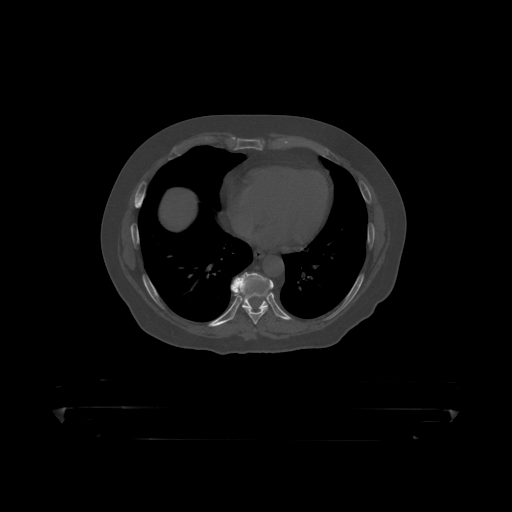
CT including the spine, one axial slice; position 249 of 390 along the scan axis; reconstruction kernel STANDARD; 120 kVp; bone window (W 1800 / L 400 HU); 1.25 mm slice thickness; 512 × 512 image matrix. Male patient, age 60 years. From the clinical record (not read from this slice): primary cancer: prostate.
Annotated regions visible in this slice (semi-automatically segmented with operator editing):
- T8 vertebra: bounding box (x1, y1, x2, y2) in pixels: (244, 280, 274, 319)
- T9 vertebra: (231, 273, 268, 309)